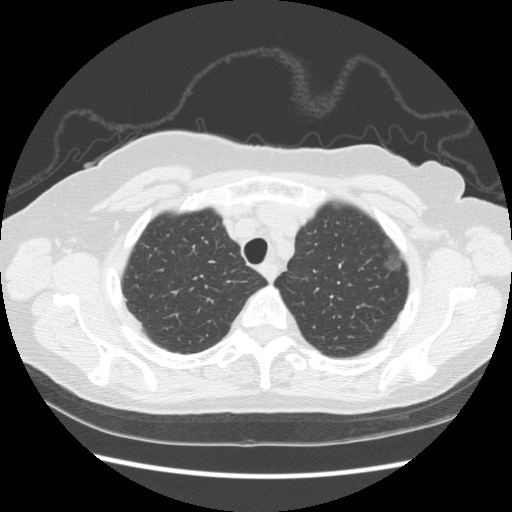
Low-dose screening chest CT, axial slice, baseline screening round, lung window (W 1500 / L -600 HU), 120 kVp, slice 32 of 247 in the series, 512 × 512 image matrix, field of view 360 × 360 mm. Female participant, aged 73 years at enrolment. Former smoker at enrolment.
- Lesion marked by an expert reader, bounding box (x1, y1, x2, y2) in pixels: (371, 232, 412, 279).
- The screening reader recorded 3 non-calcified nodules or masses ≥4 mm on this exam (left upper lobe, left upper lobe, left upper lobe); which of them this box marks is not recorded.
- Official screen result: positive, change unspecified: nodule(s) >= 4 mm or enlarging nodule(s), mass(es), or other non-specific abnormalities suspicious for lung cancer.